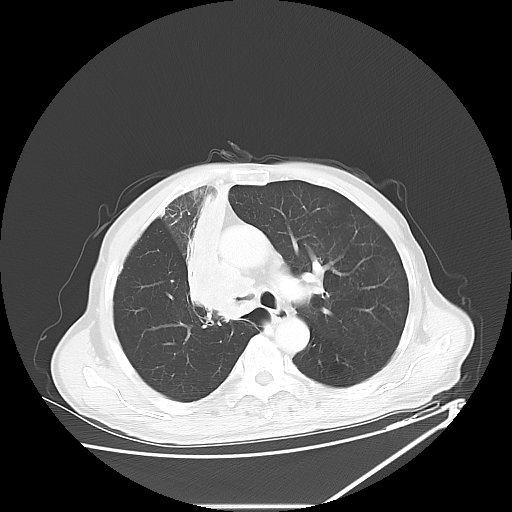
Chest CT, one axial slice. Slice 41 of 60 in the series (ordered by position). Reconstruction kernel LUNG. Lung window (W 1500 / L -600 HU). 5 mm slice thickness. 512 × 512 image matrix. Male patient, age 73 years. From the clinical record (not read from this slice): clinical TNM (as recorded): T2a N1 M0.
Structures marked on this image (rectangle marked by the reading radiologist):
- lung tumour (recorded histology: squamous cell carcinoma): bounding box <179,186,243,338> (left, top, right, bottom; pixels)